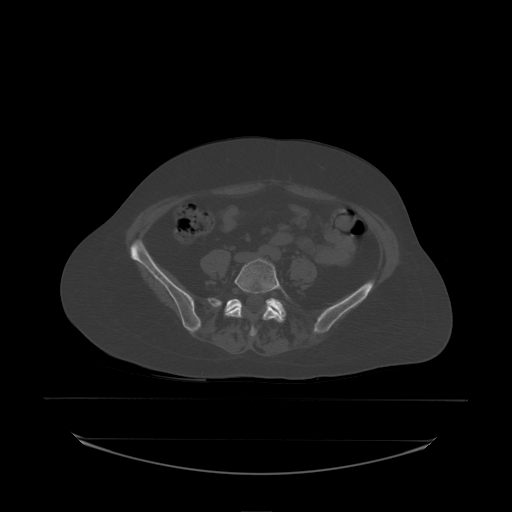
CT including the spine, one axial slice. Slice 37 of 242 in the series (ordered by position). Bone window (W 1800 / L 400 HU). 2.5 mm slice thickness. 512 × 512 image matrix, field of view 500 × 500 mm. Patient: female, 53 years. From the clinical record (not read from this slice): primary cancer: lung.
Outlined on this slice (semi-automatic segmentation, software-assisted and operator-edited):
- L5 vertebra: bounding box [x1, y1, x2, y2] px = [225, 259, 288, 337]